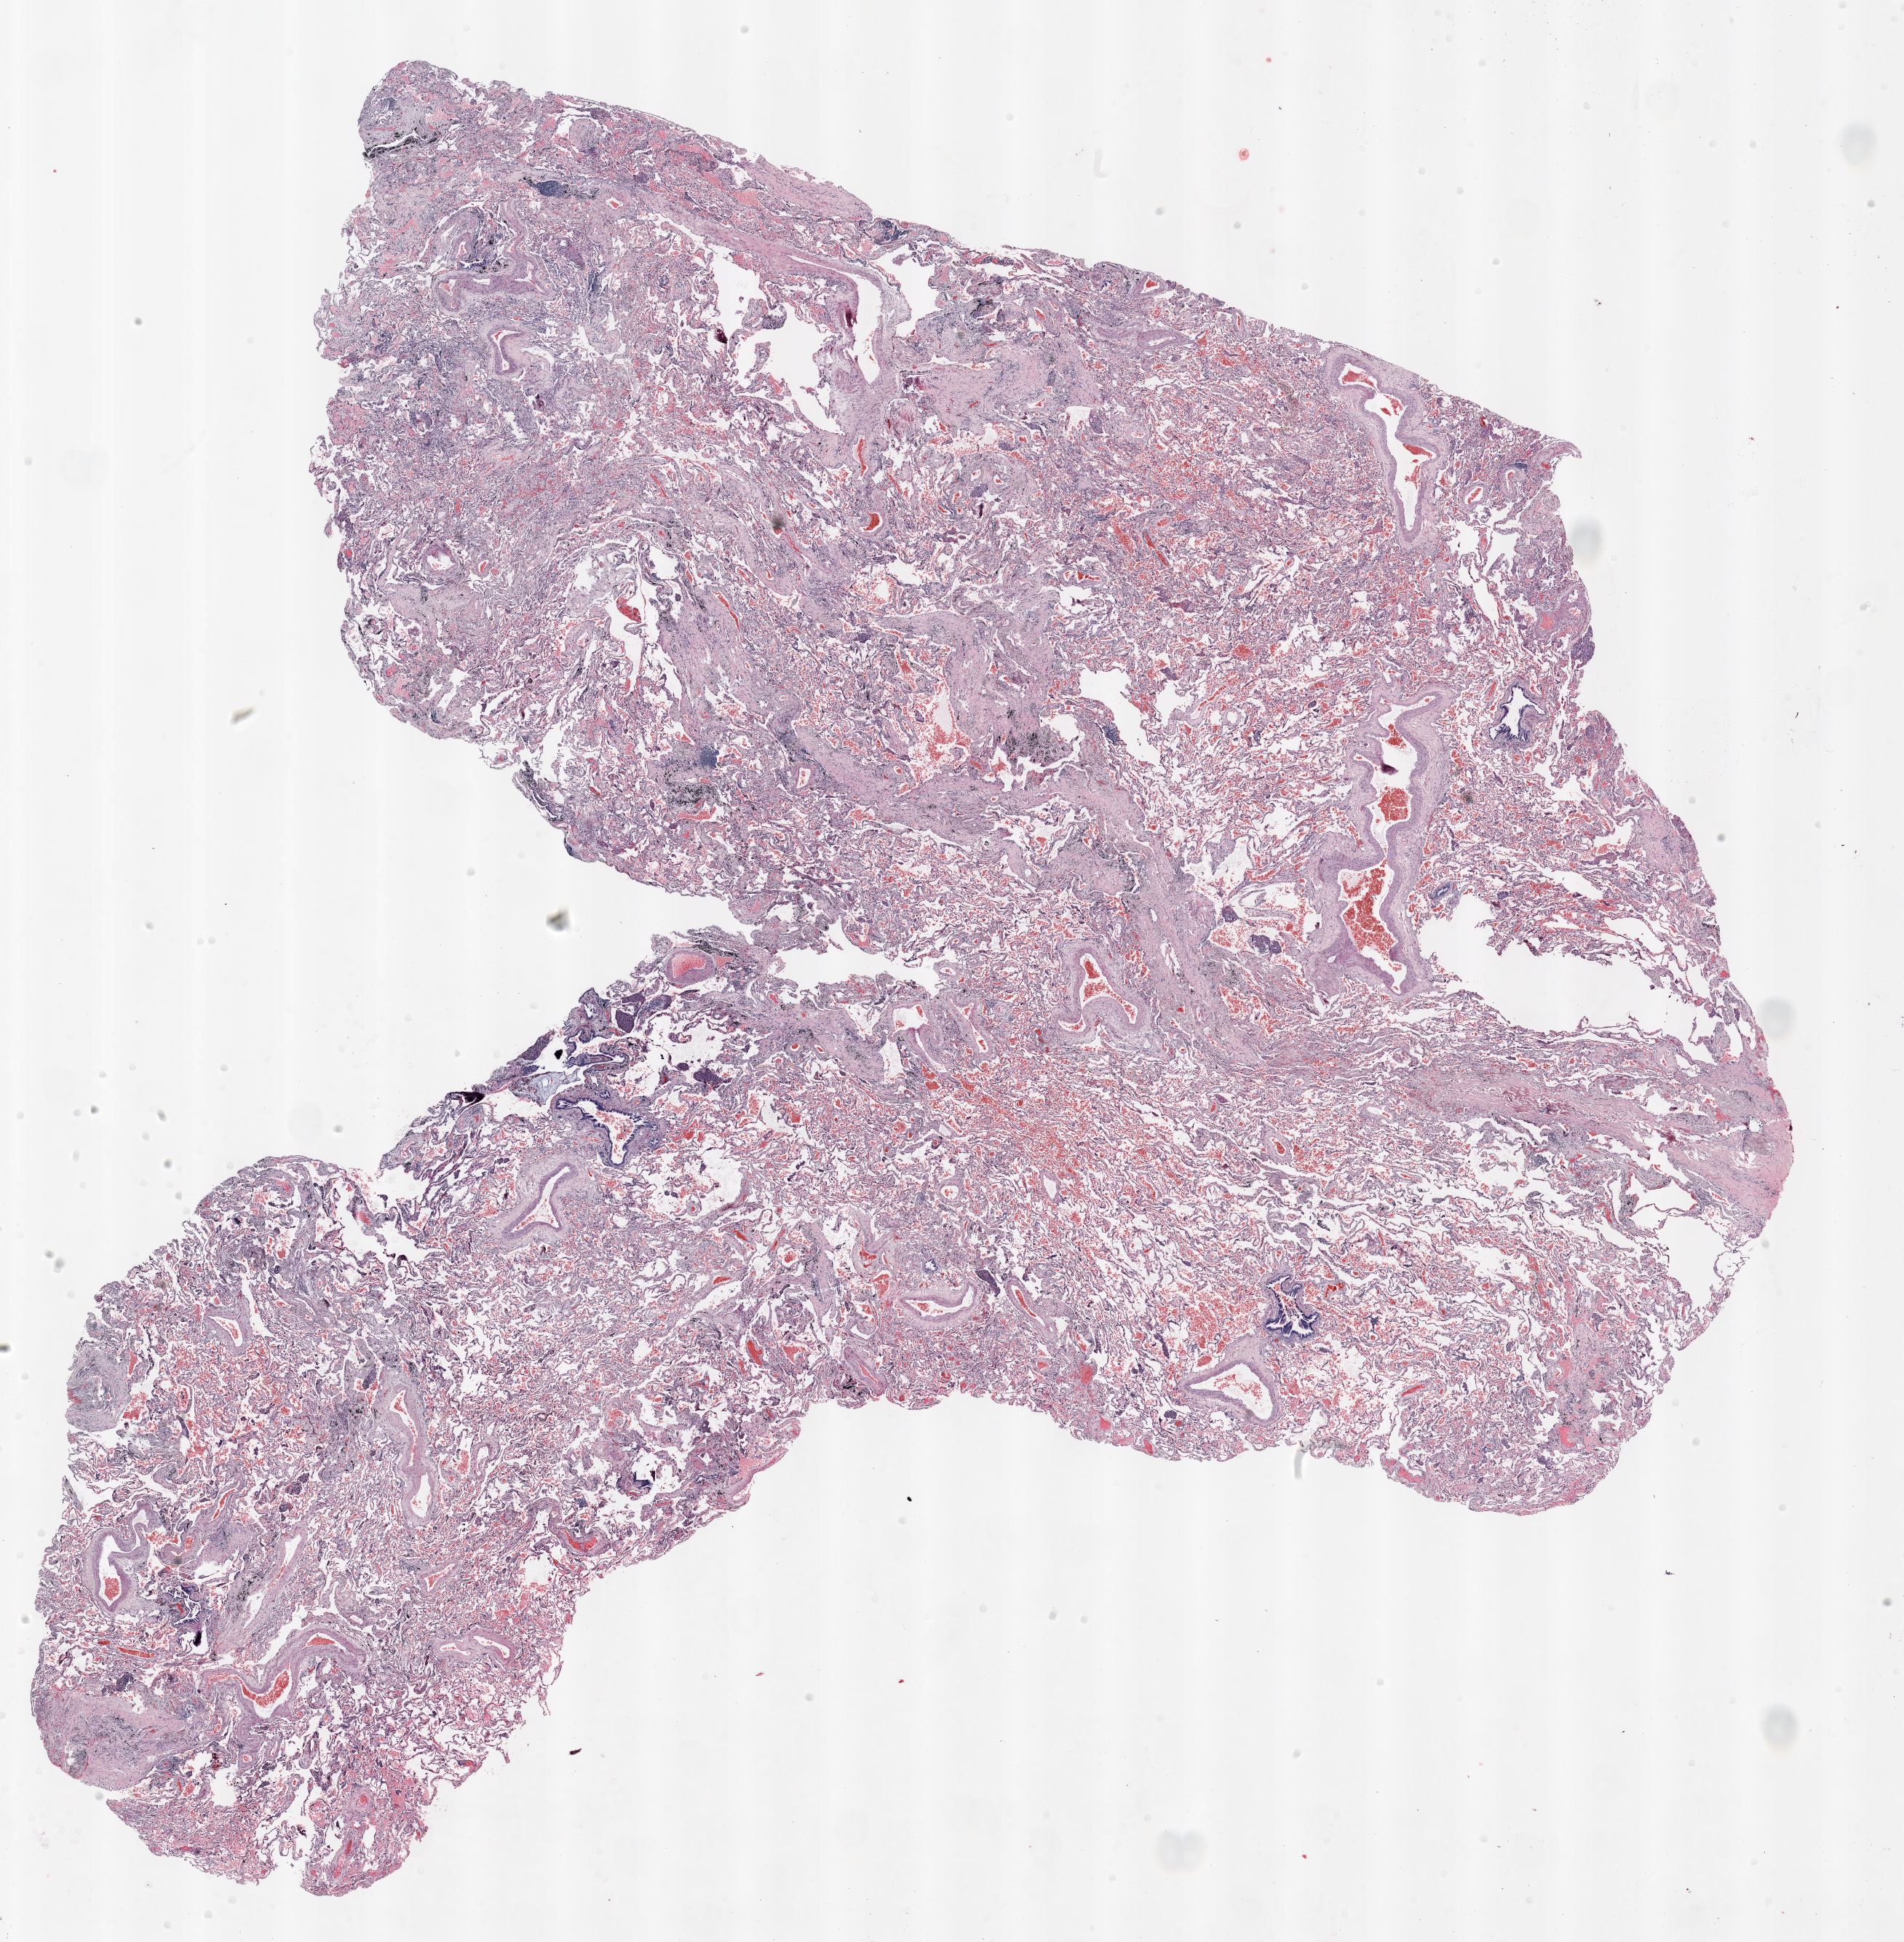
H&E-stained whole-slide image, a low-resolution overview of the entire scanned area, about 21.0 x 21.4 mm (acquisition: 20x scan); FFPE section; lung tissue. Male patient, aged 58 at enrolment. Former smoker at enrolment. Grade: moderately differentiated (G2).
Stage (AJCC 6th edition): IB. Participant's lung-cancer diagnosis: Squamous cell carcinoma, NOS (ICD-O-3 8070/3). Primary tumour location (clinical record): right upper lobe. Tumour size (pathology): 18 mm. ICD-O-3 topography: upper lobe of lung (C34.1).